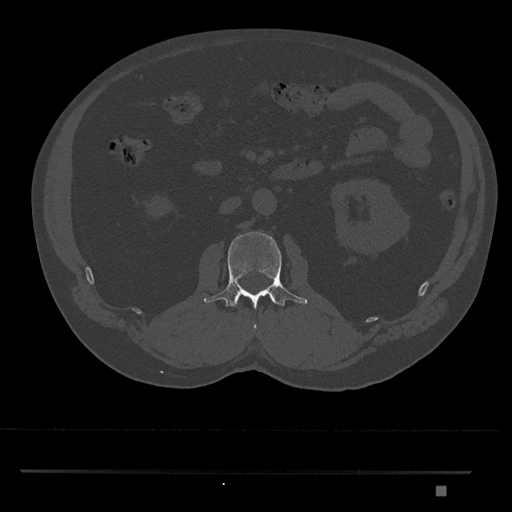
CT including the spine, one axial slice. Slice 757 of 1134 in the series (ordered by position). Reconstruction kernel Br40s/3. 120 kVp. Bone window (W 1800 / L 400 HU). 0.5 mm slice thickness. 512 × 512 image matrix, field of view 429 × 429 mm. Patient: male, 65 years. Case-level facts recorded for this patient, not image findings: primary cancer: prostate.
Annotated regions visible in this slice (semi-automatic segmentation, software-assisted and operator-edited):
- L2 vertebra: bounding box <203,231,308,329> (left, top, right, bottom; pixels)